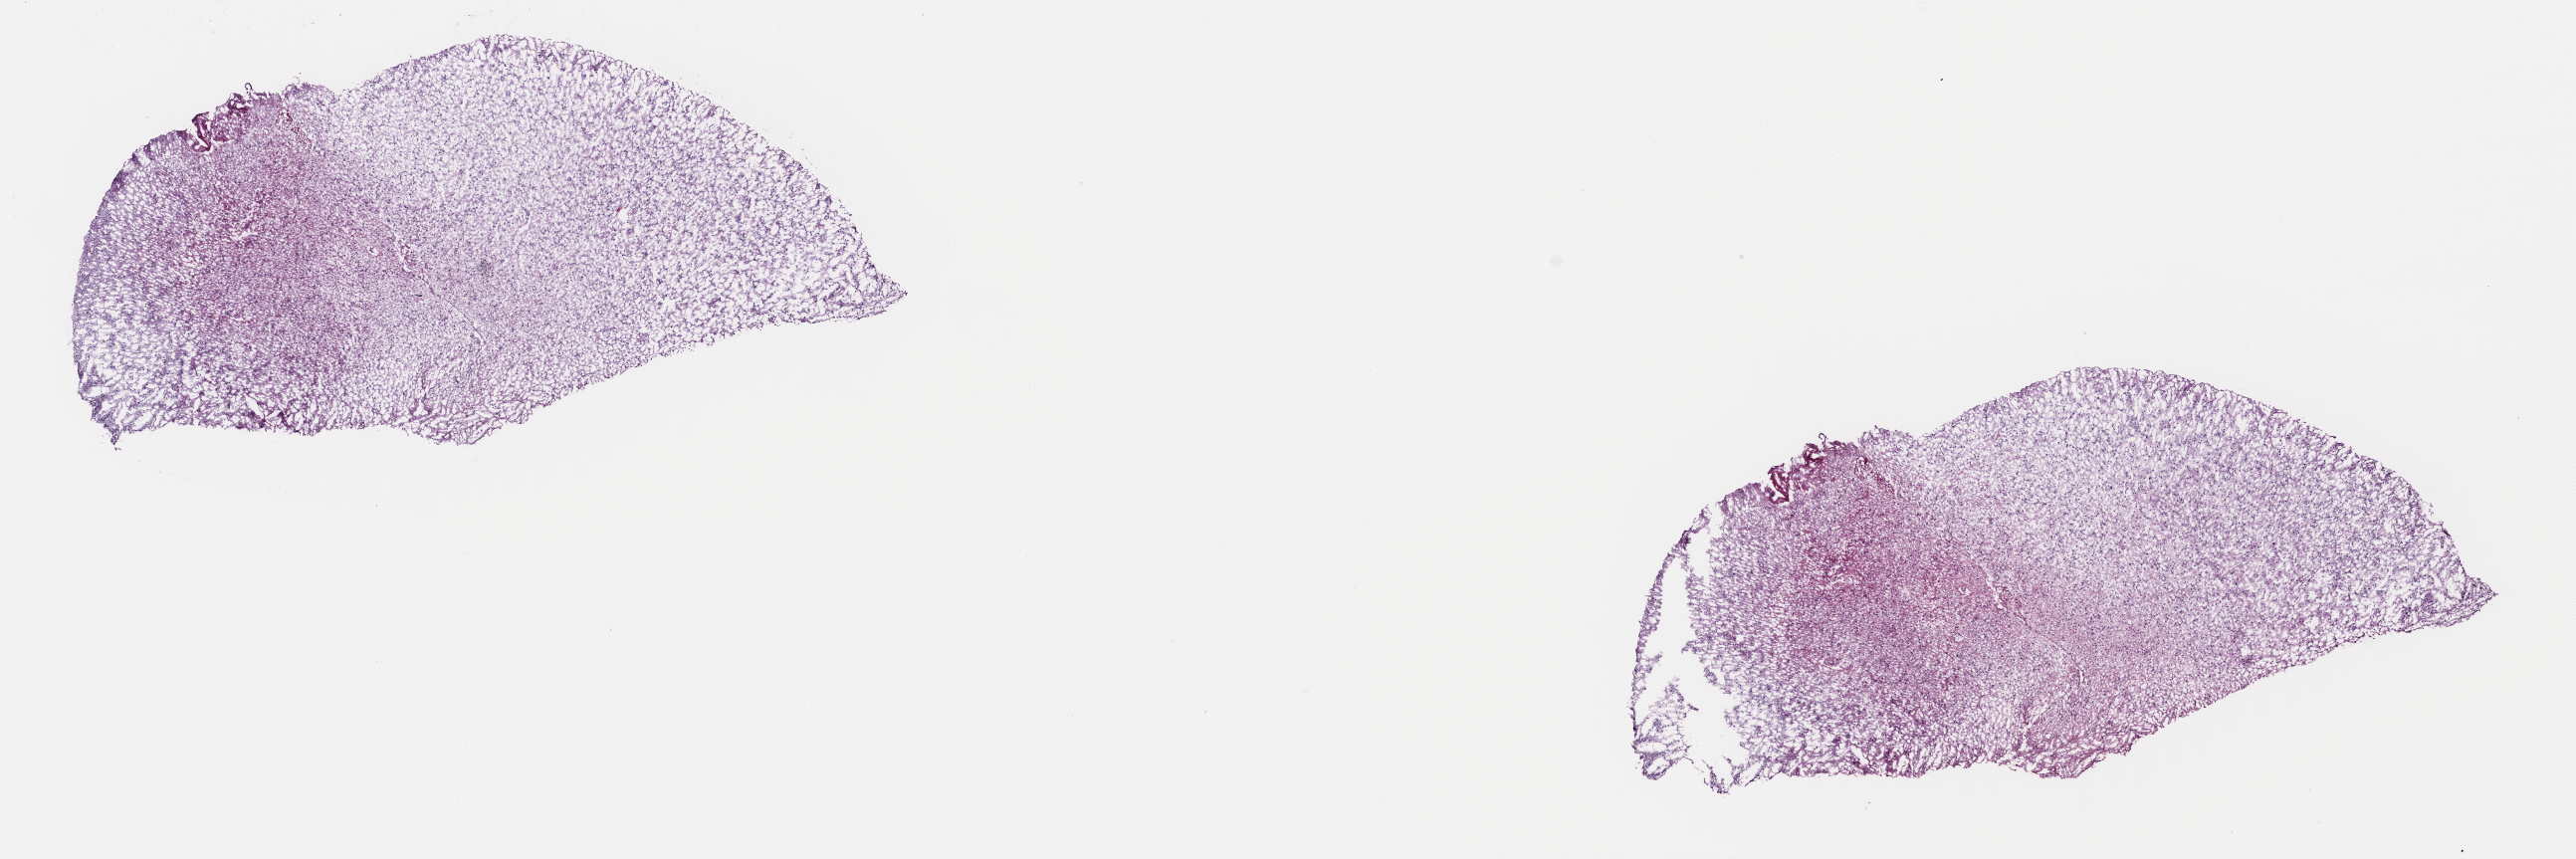
H&E whole-slide image — a low-resolution overview of the entire scanned area, about 20.3 x 6.8 mm (slide scanned at 40x), frozen section, brain, primary tumour sample. Male, age 29 years at initial diagnosis. Histologic grade: G2 (moderately differentiated). Pathologist review of this section (percent, as recorded): tumour cells 40%, tumour nuclei 80%, normal cells 10%, stromal cells 50%, necrosis 0%. Infiltration values recorded for this section: lymphocyte infiltration 0%, monocyte infiltration 0%, neutrophil infiltration 0%.
Diagnosis: Astrocytoma, NOS (cerebrum).